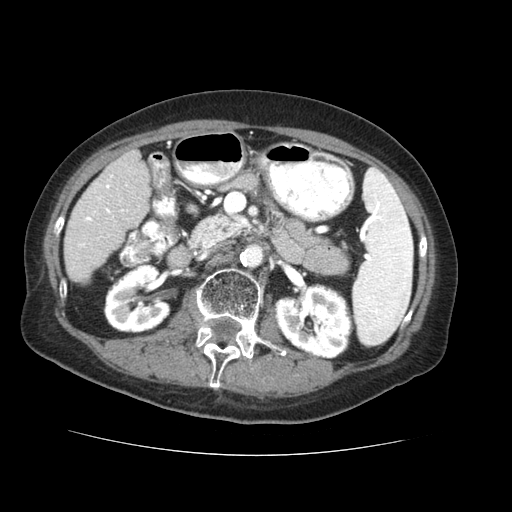
Contrast-enhanced abdominal CT (liver protocol), one axial slice; position 15 of 73 along the scan axis; reconstruction kernel STANDARD; soft-tissue window (W 400 / L 40 HU); 2.5 mm slice thickness; 512 × 512 image matrix, field of view 360 × 360 mm. From the clinical record (not read from this slice): diagnosis: hepatocellular carcinoma (patient treated with transarterial chemoembolisation; whether this scan precedes or follows treatment is not stated here); TNM stage (as recorded): Stage-IVB; Child-Pugh class: A; tumour differentiation: well differentiated; tumour nodularity: uninodular.
Structures marked on this image (semi-automatically segmented with operator editing):
- liver parenchyma outside the tumour (the mass and vessels are separate outlines, so this box may not span the whole liver): box from (x=64, y=150) to (x=150, y=282) px
- liver vessels: (x=78, y=175)–(x=127, y=248)